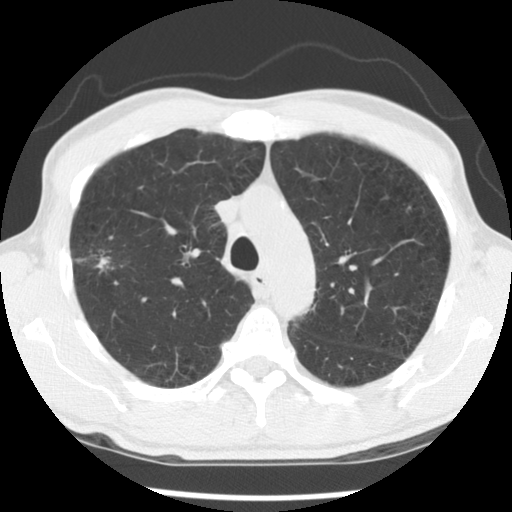
Low-dose screening chest CT, axial slice, second annual screen, lung window (W 1500 / L -600 HU), 2.5 mm slice thickness, 140 kVp. Male participant, aged 56 years at enrolment. Current smoker at enrolment.
• Lesion marked by an expert reader, bounding box (x1, y1, x2, y2) in pixels: (57, 230, 143, 299).
• Reader record for this screening exam (exam-level; its link to the box is not recorded): non-calcified nodule or mass ≥4 mm, right upper lobe, 30 × 18 mm, spiculated (stellate) margins, mixed attenuation, pre-existing on the prior screen: yes; interval growth: yes.
• Later outcome: lung cancer diagnosed 326 days after this screen — squamous cell carcinoma, NOS, right upper lobe, right middle lobe, moderately differentiated (G2), stage IB (AJCC 6th edition), 70 mm at pathology.